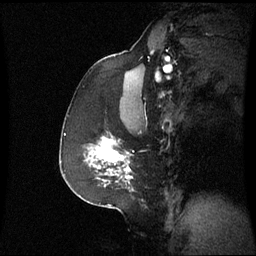
Breast MRI (dynamic contrast-enhanced), one sagittal slice; position 39 of 60 along the scan axis; dynamic contrast-enhanced series, image 2 of 3 at this slice position (ordered by acquisition); 1.5 T; TE 4.2 ms, TR 8.9 ms; 2.4 mm slice thickness; 256 × 256 image matrix, field of view 230 × 230 mm. Patient: female, 59 years. From the clinical record (not read from this slice): setting: breast cancer imaged before/during neoadjuvant chemotherapy; receptor status: triple-negative.
Structures marked on this image (semi-automatically segmented with operator editing):
- analysis volume of interest (the breast-tissue region the enhancement analysis was run in; not a lesion): bounding box [x1, y1, x2, y2] px = [86, 135, 133, 183]
- tumour enhancement mask (voxels above the 70 % enhancement threshold inside the analysis volume of interest): [96, 138, 131, 178]